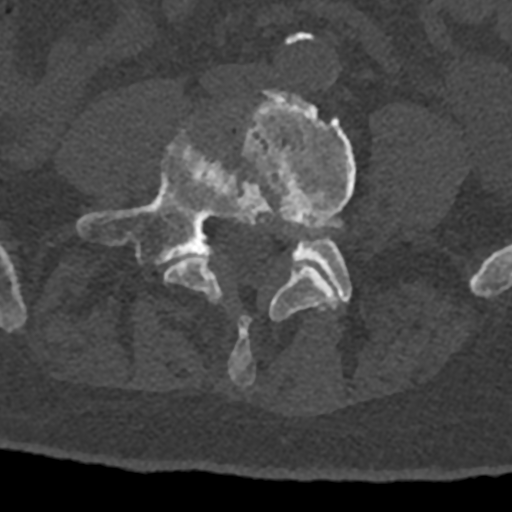
CT including the spine, one axial slice; slice 228 of 797 in the series (ordered by position); bone window (W 1800 / L 400 HU); 0.5 mm slice thickness; 512 × 512 image matrix. Male patient, age 74 years. From the clinical record (not read from this slice): primary cancer: renal; vertebrae with lytic lesions (as recorded): T10, L1, L2, L3, L4, L5.
Structures marked on this image (semi-automatically segmented with operator editing):
- L4 vertebra: box from (x=163, y=90) to (x=356, y=385) px
- L5 vertebra: (x=77, y=131)–(x=352, y=303)